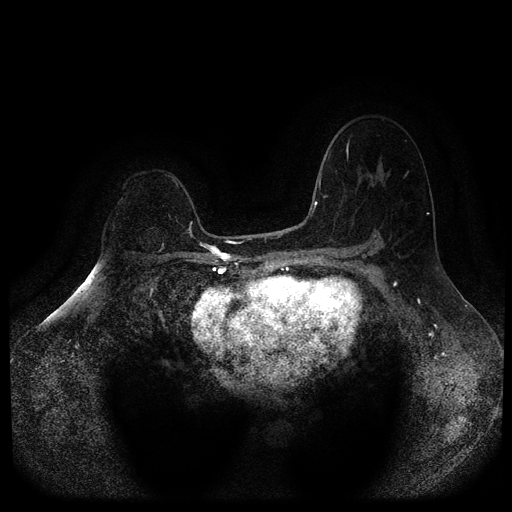
Breast MRI (dynamic contrast-enhanced, multi-phase), one axial slice. Position 71 of 116 along the scan axis. Dynamic contrast-enhanced series, time point 2 of 5 at this slice position (early post-contrast). 1.5 T. TE 2.6 ms, TR 5.4 ms. 512 × 512 image matrix, field of view 340 × 340 mm. Patient: female, 64 years.
Outlined on this slice (semi-automatic segmentation, software-assisted and operator-edited):
- breast lesion (labelled benign in the annotation): bounding box [x1, y1, x2, y2] px = [139, 227, 165, 253]